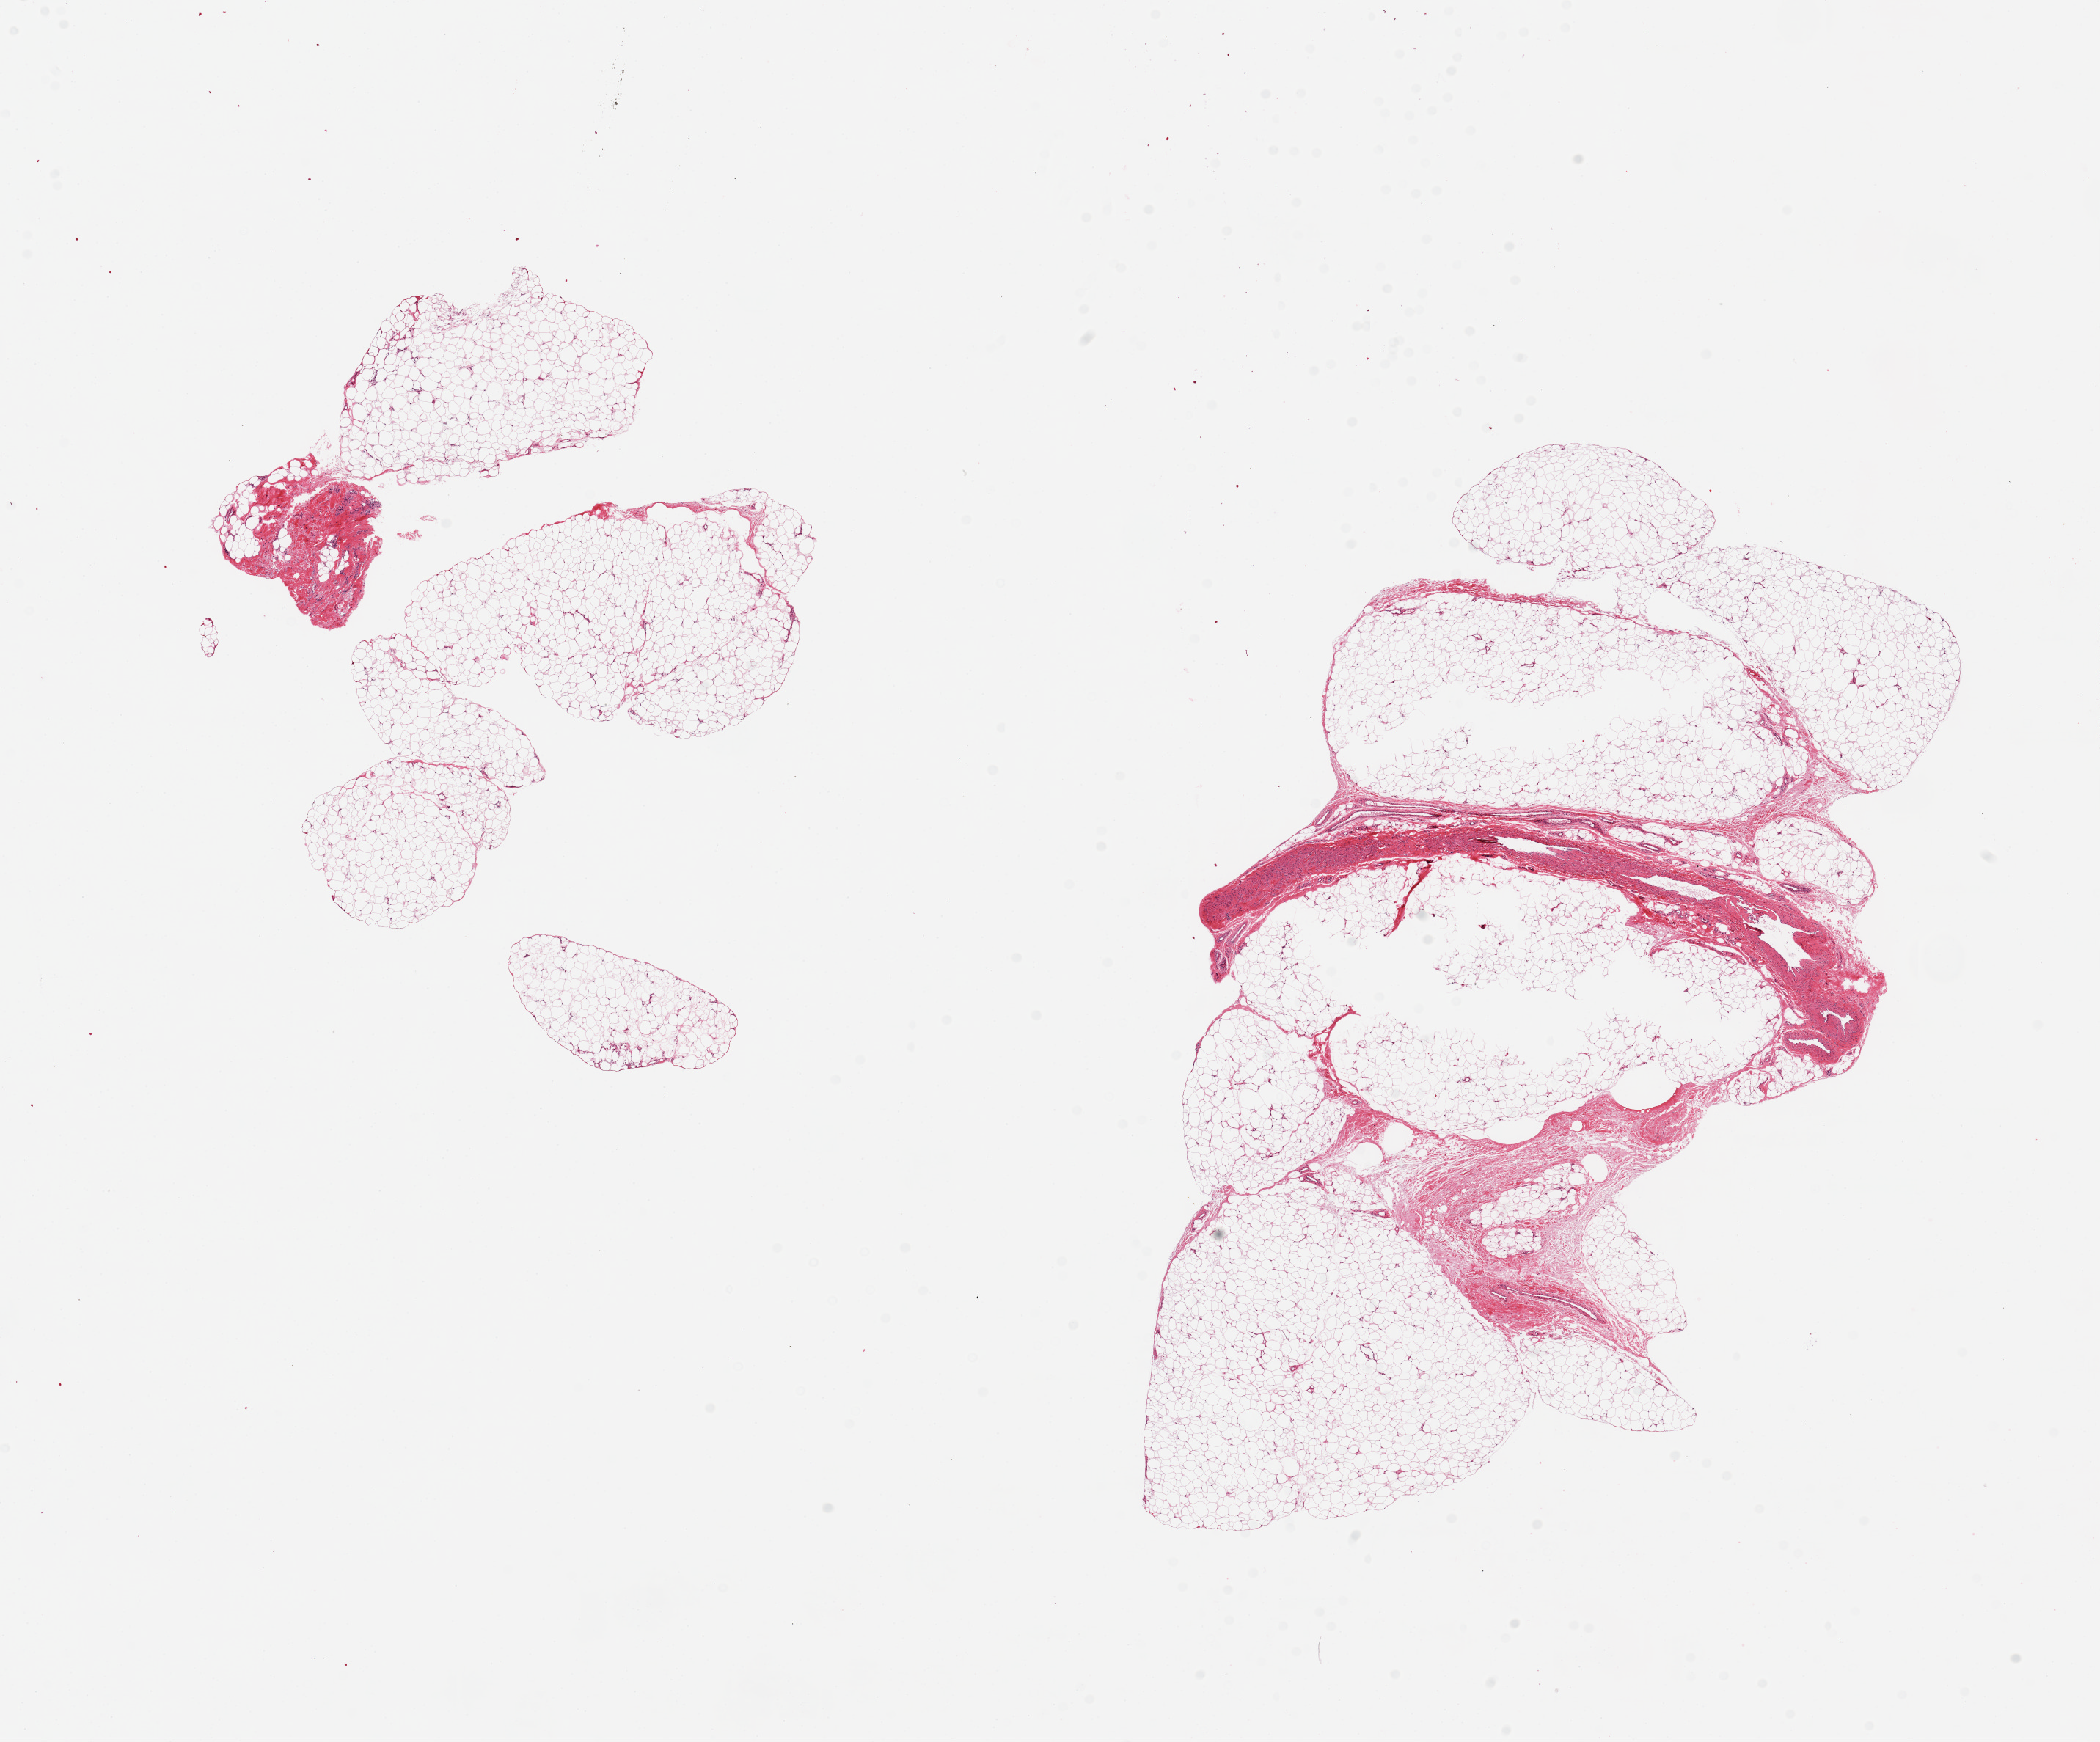
Digitized haematoxylin and eosin-stained section, brightfield — low-resolution overview of the scanned area, about 22.6 x 18.8 mm (from a 20x scan), PAXgene-fixed paraffin-embedded (PFPE) section, target tissue: adipose tissue, tissue donor sample. Donor: male.
* pathologist's review note for this sample: 2 pieces ~10x6mm, fibrous bands noted